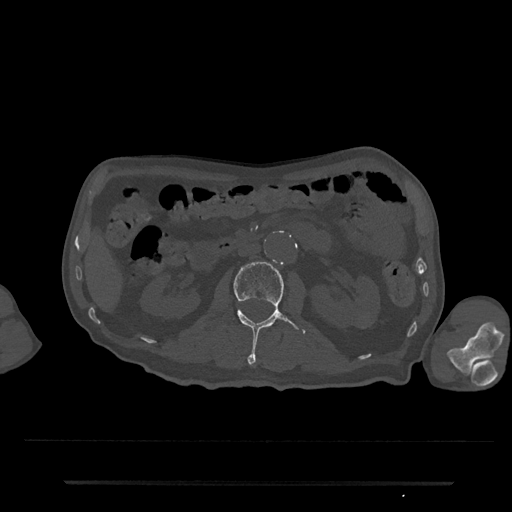
CT including the spine, one axial slice. Position 58 of 797 along the scan axis. Reconstruction kernel Br40s/3. Bone window (W 1800 / L 400 HU). 512 × 512 image matrix, field of view 427 × 427 mm. Male patient, age 74 years. Case-level facts recorded for this patient, not image findings: primary cancer: prostate.
Annotated regions visible in this slice (semi-automatically segmented with operator editing):
- L2 vertebra: bounding box (x1, y1, x2, y2) in pixels: (234, 262, 306, 364)